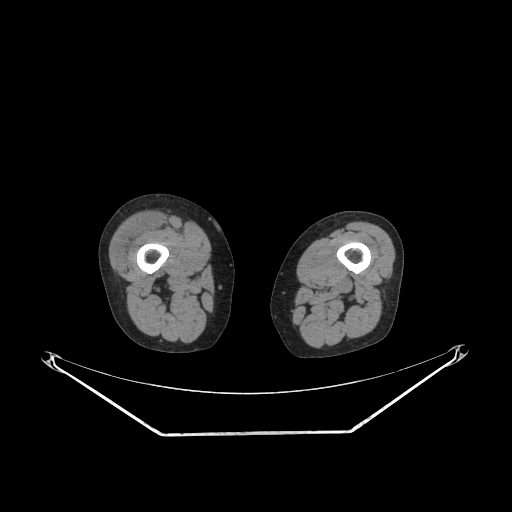
CT of an extremity soft-tissue mass (from a PET/CT study), one axial slice; slice 209 of 311 in the series (ordered by position); 140 kVp; soft-tissue window (W 400 / L 40 HU); 3.75 mm slice thickness; 512 × 512 image matrix, field of view 500 × 500 mm. Female patient. From the clinical record (not read from this slice): histological type: pleiomorphic undifferentiated sarcoma; grade: high; site of the primary tumour: right quadricep.
Structures marked on this image (expert contour drawn on MRI and transferred to this co-registered scan by the dataset authors):
- tumour plus oedema (research contour): bounding box (x1, y1, x2, y2) in pixels: (133, 212, 159, 225)